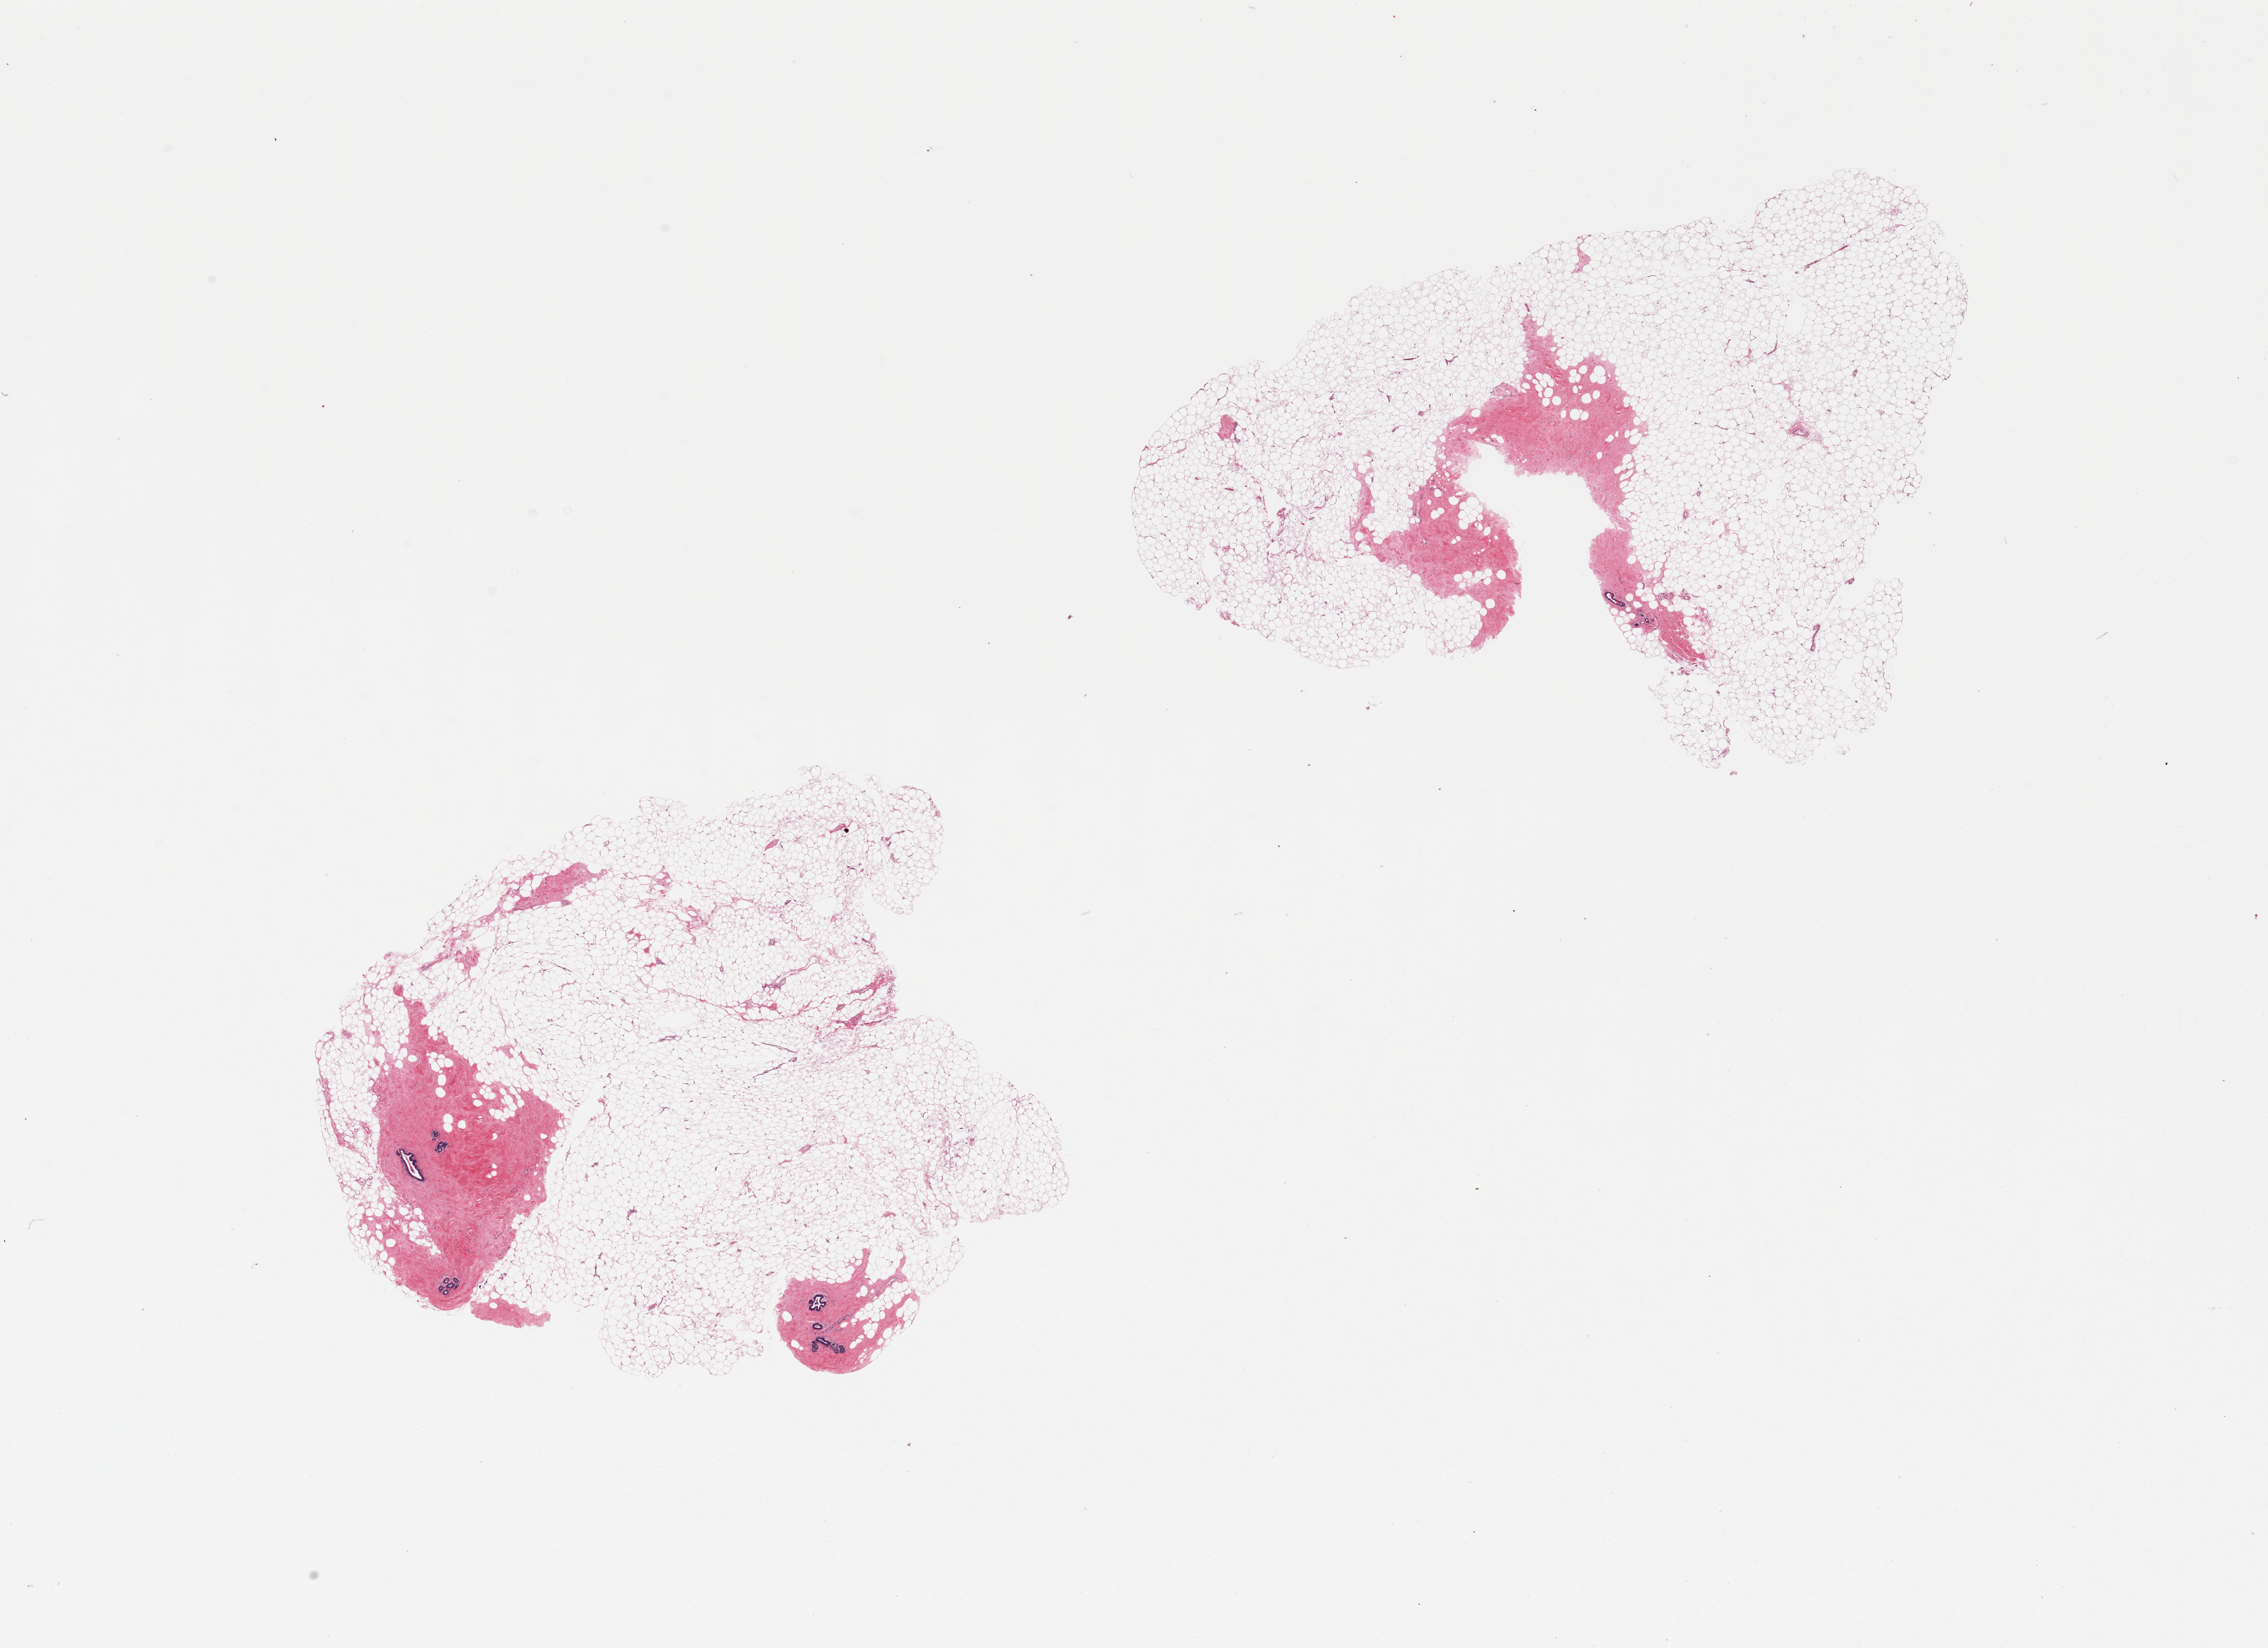
Whole-slide image, haematoxylin and eosin stain, shown as a low-resolution overview of the whole scanned area (about 25.6 x 18.6 mm, slide scanned at 20x), PAXgene-fixed paraffin-embedded (PFPE) section, sampled site (target tissue): breast, tissue donor sample. Female donor.
Reviewer comment on this tissue sample: 2 pieces, each ~90% fat, ductal elements present.